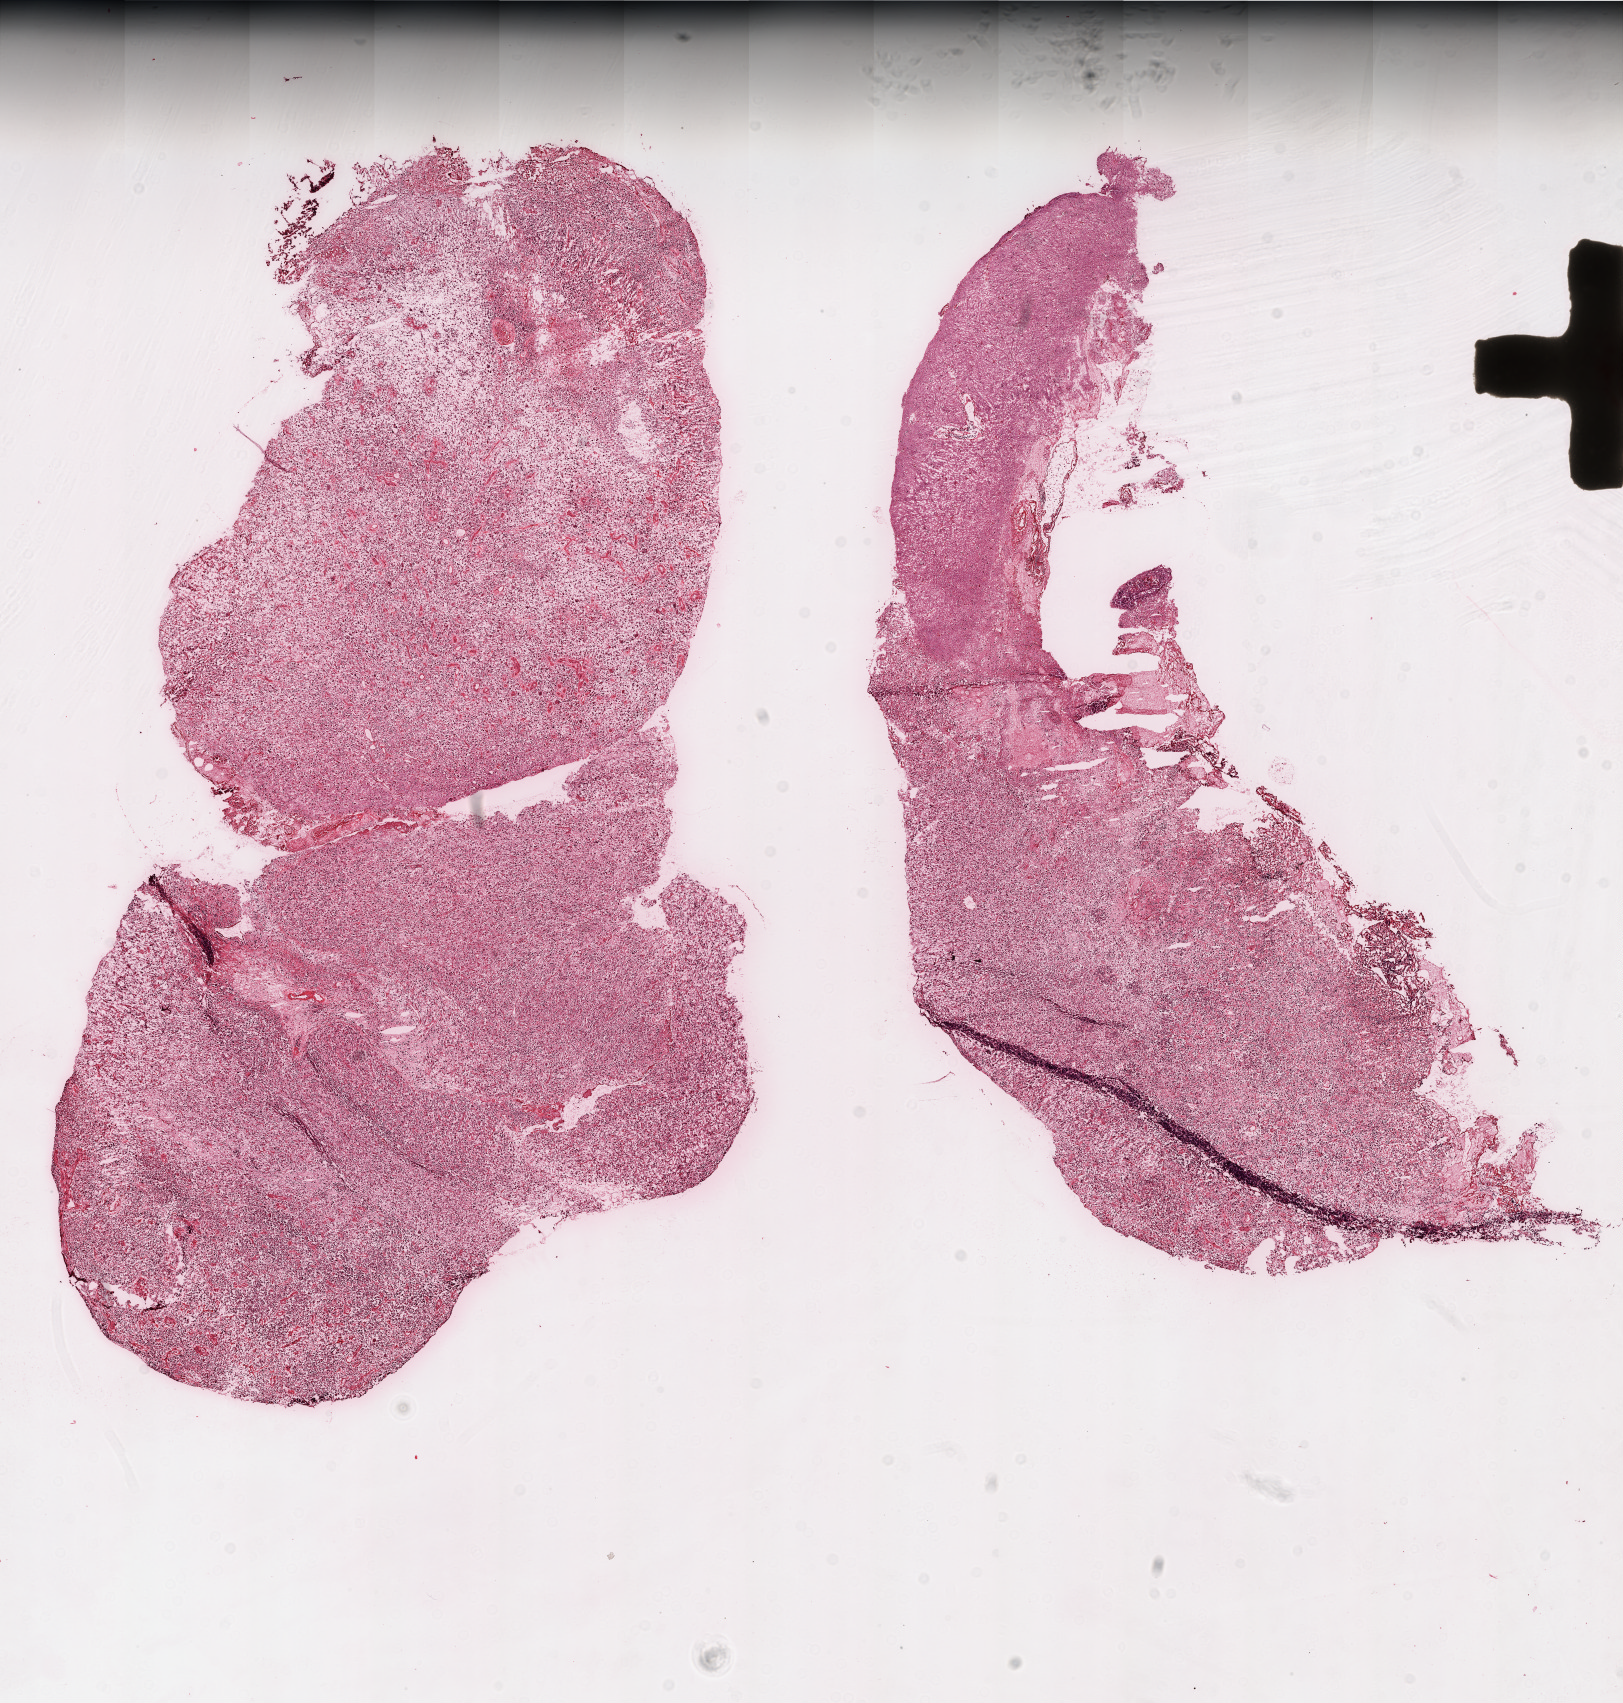
Hematoxylin and eosin (H&E) stained whole-slide image — a low-resolution overview of the entire scanned area, about 13.0 x 13.6 mm (slide scanned at 20x); frozen section from the top of the tissue portion; primary tumour sample from the brain. Female patient; age at initial diagnosis 69 years. Slide review estimates, as recorded: tumour cells 80%, tumour nuclei 95%, normal cells 10%, stromal cells 5%, necrosis 5%.
Histologic diagnosis: Glioblastoma.